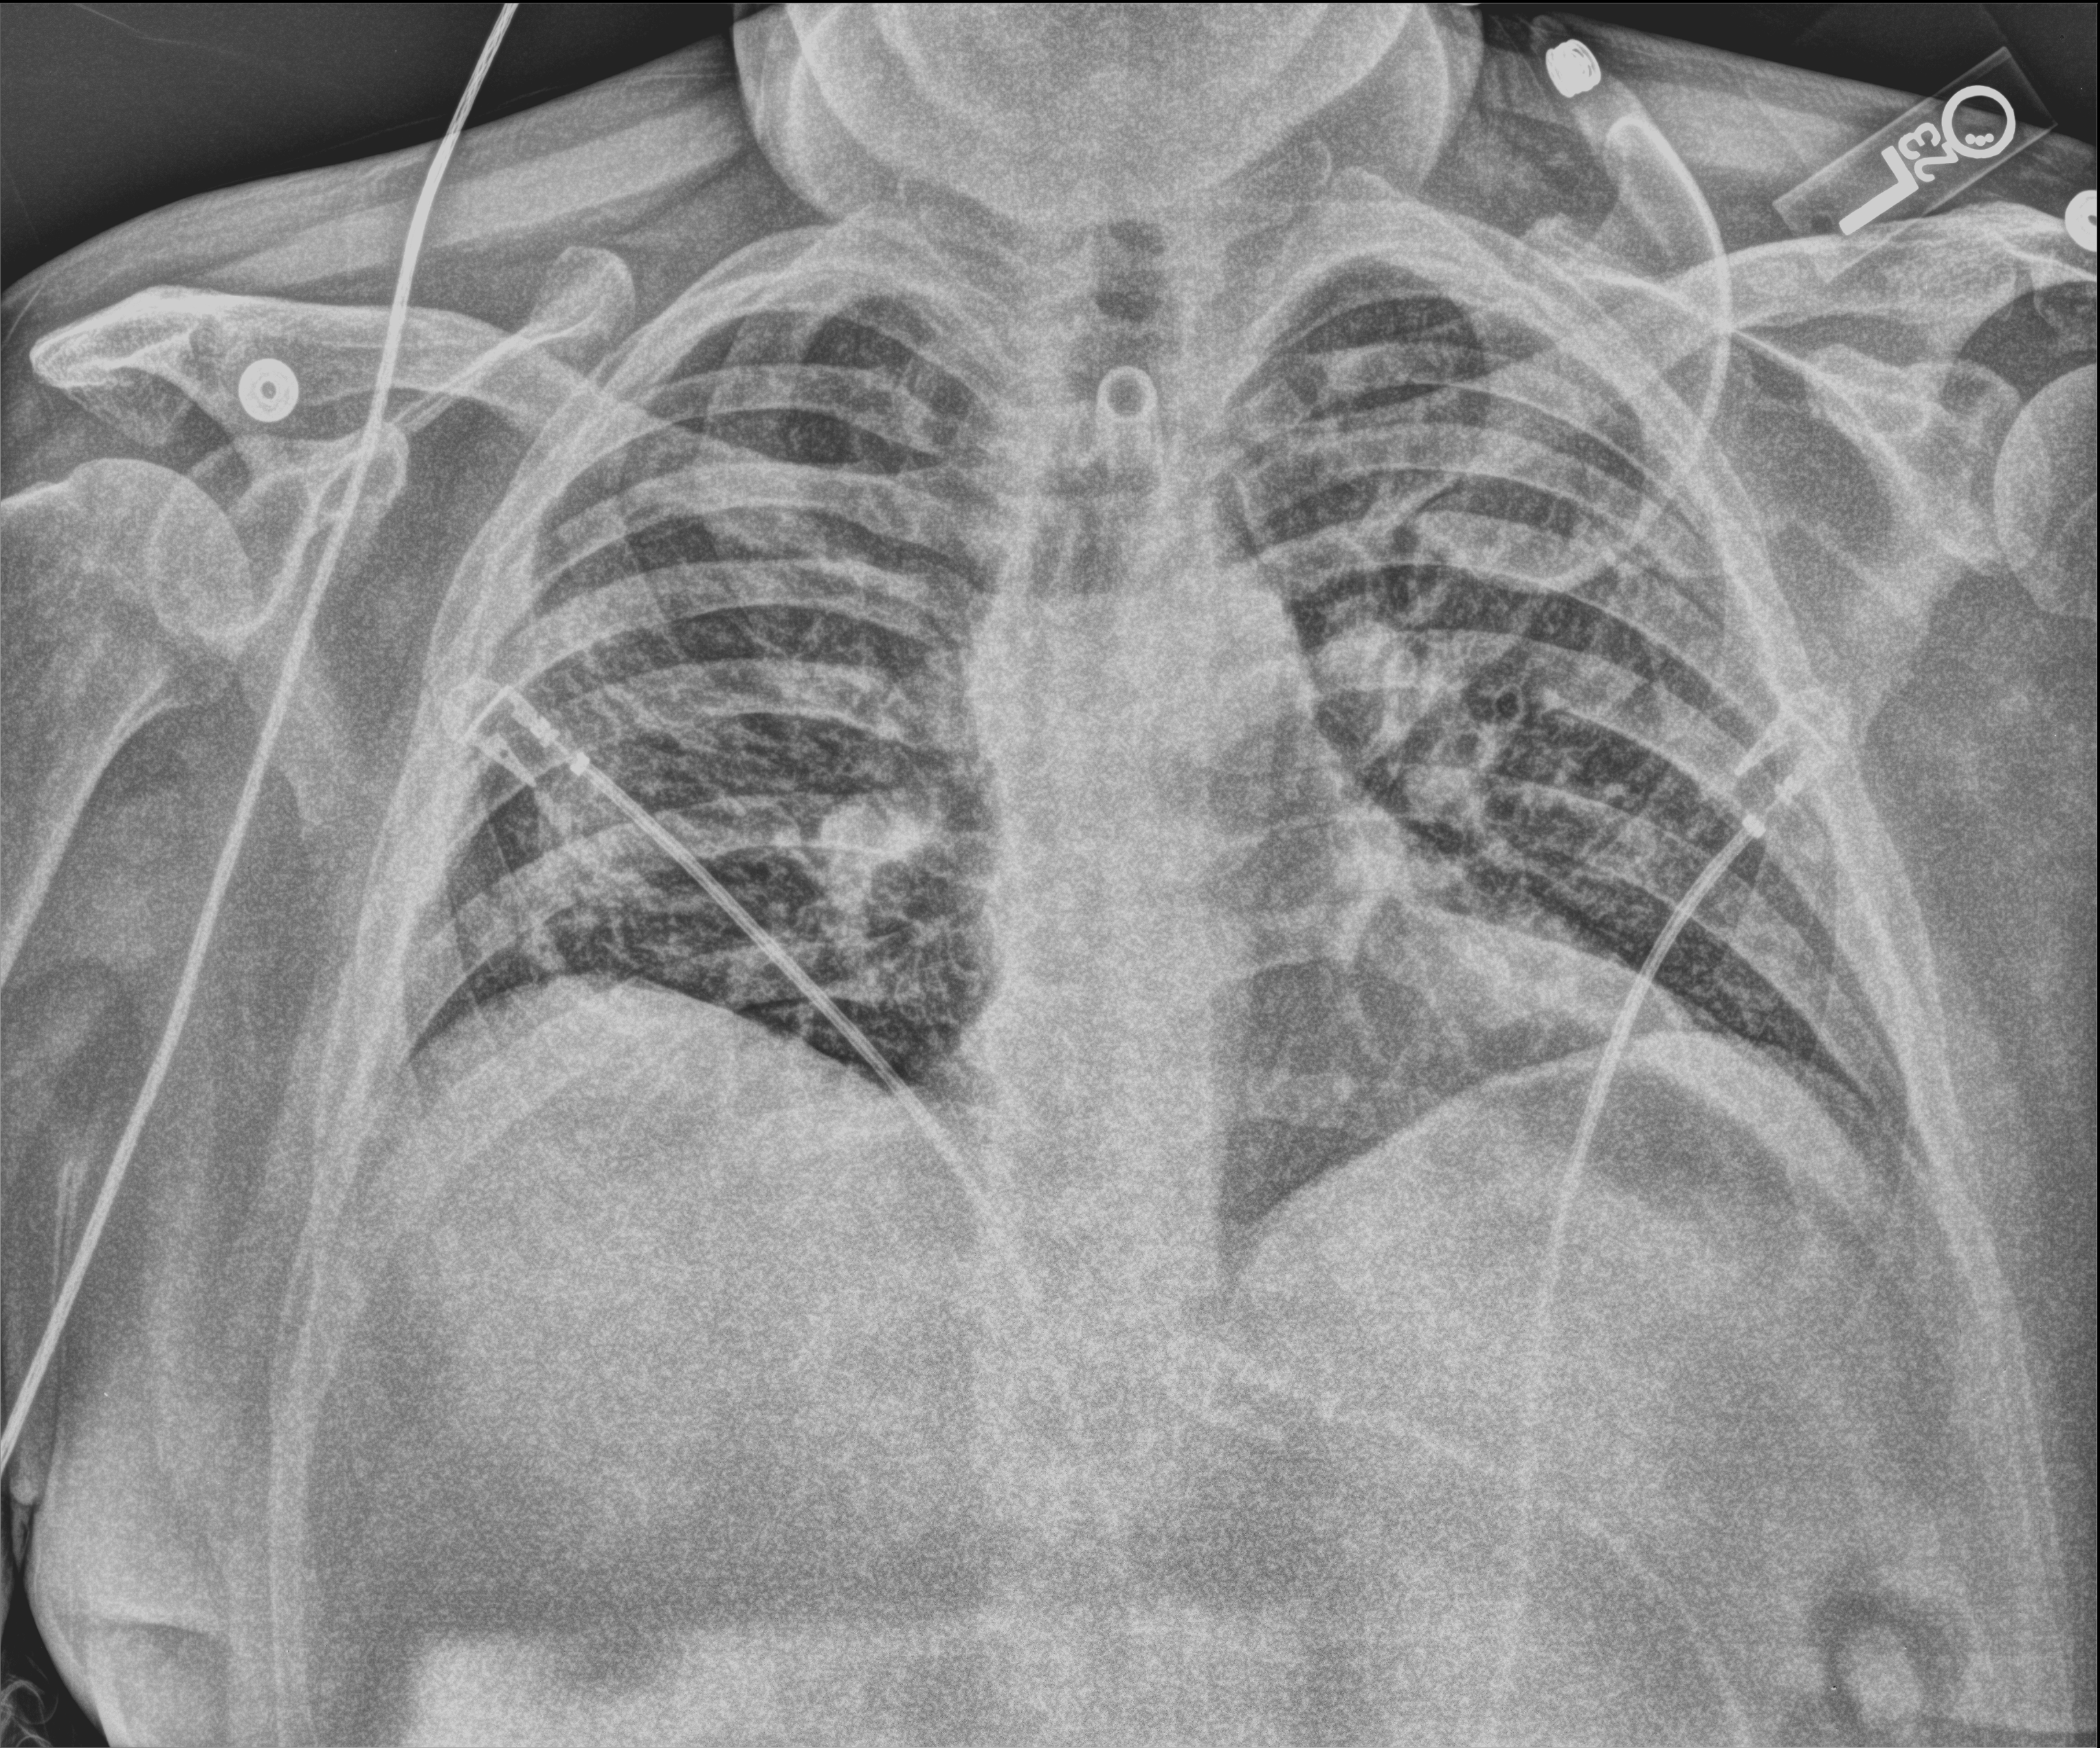
Bedside chest radiograph (computed radiography); anteroposterior (AP) projection. Male patient hospitalised with COVID-19, age 18–59 years.
From the hospital-stay record, not from the radiograph (when in the stay this image was taken is not recorded):
- chronic kidney disease (admission record): no
- admitted to intensive care during this hospital stay: yes